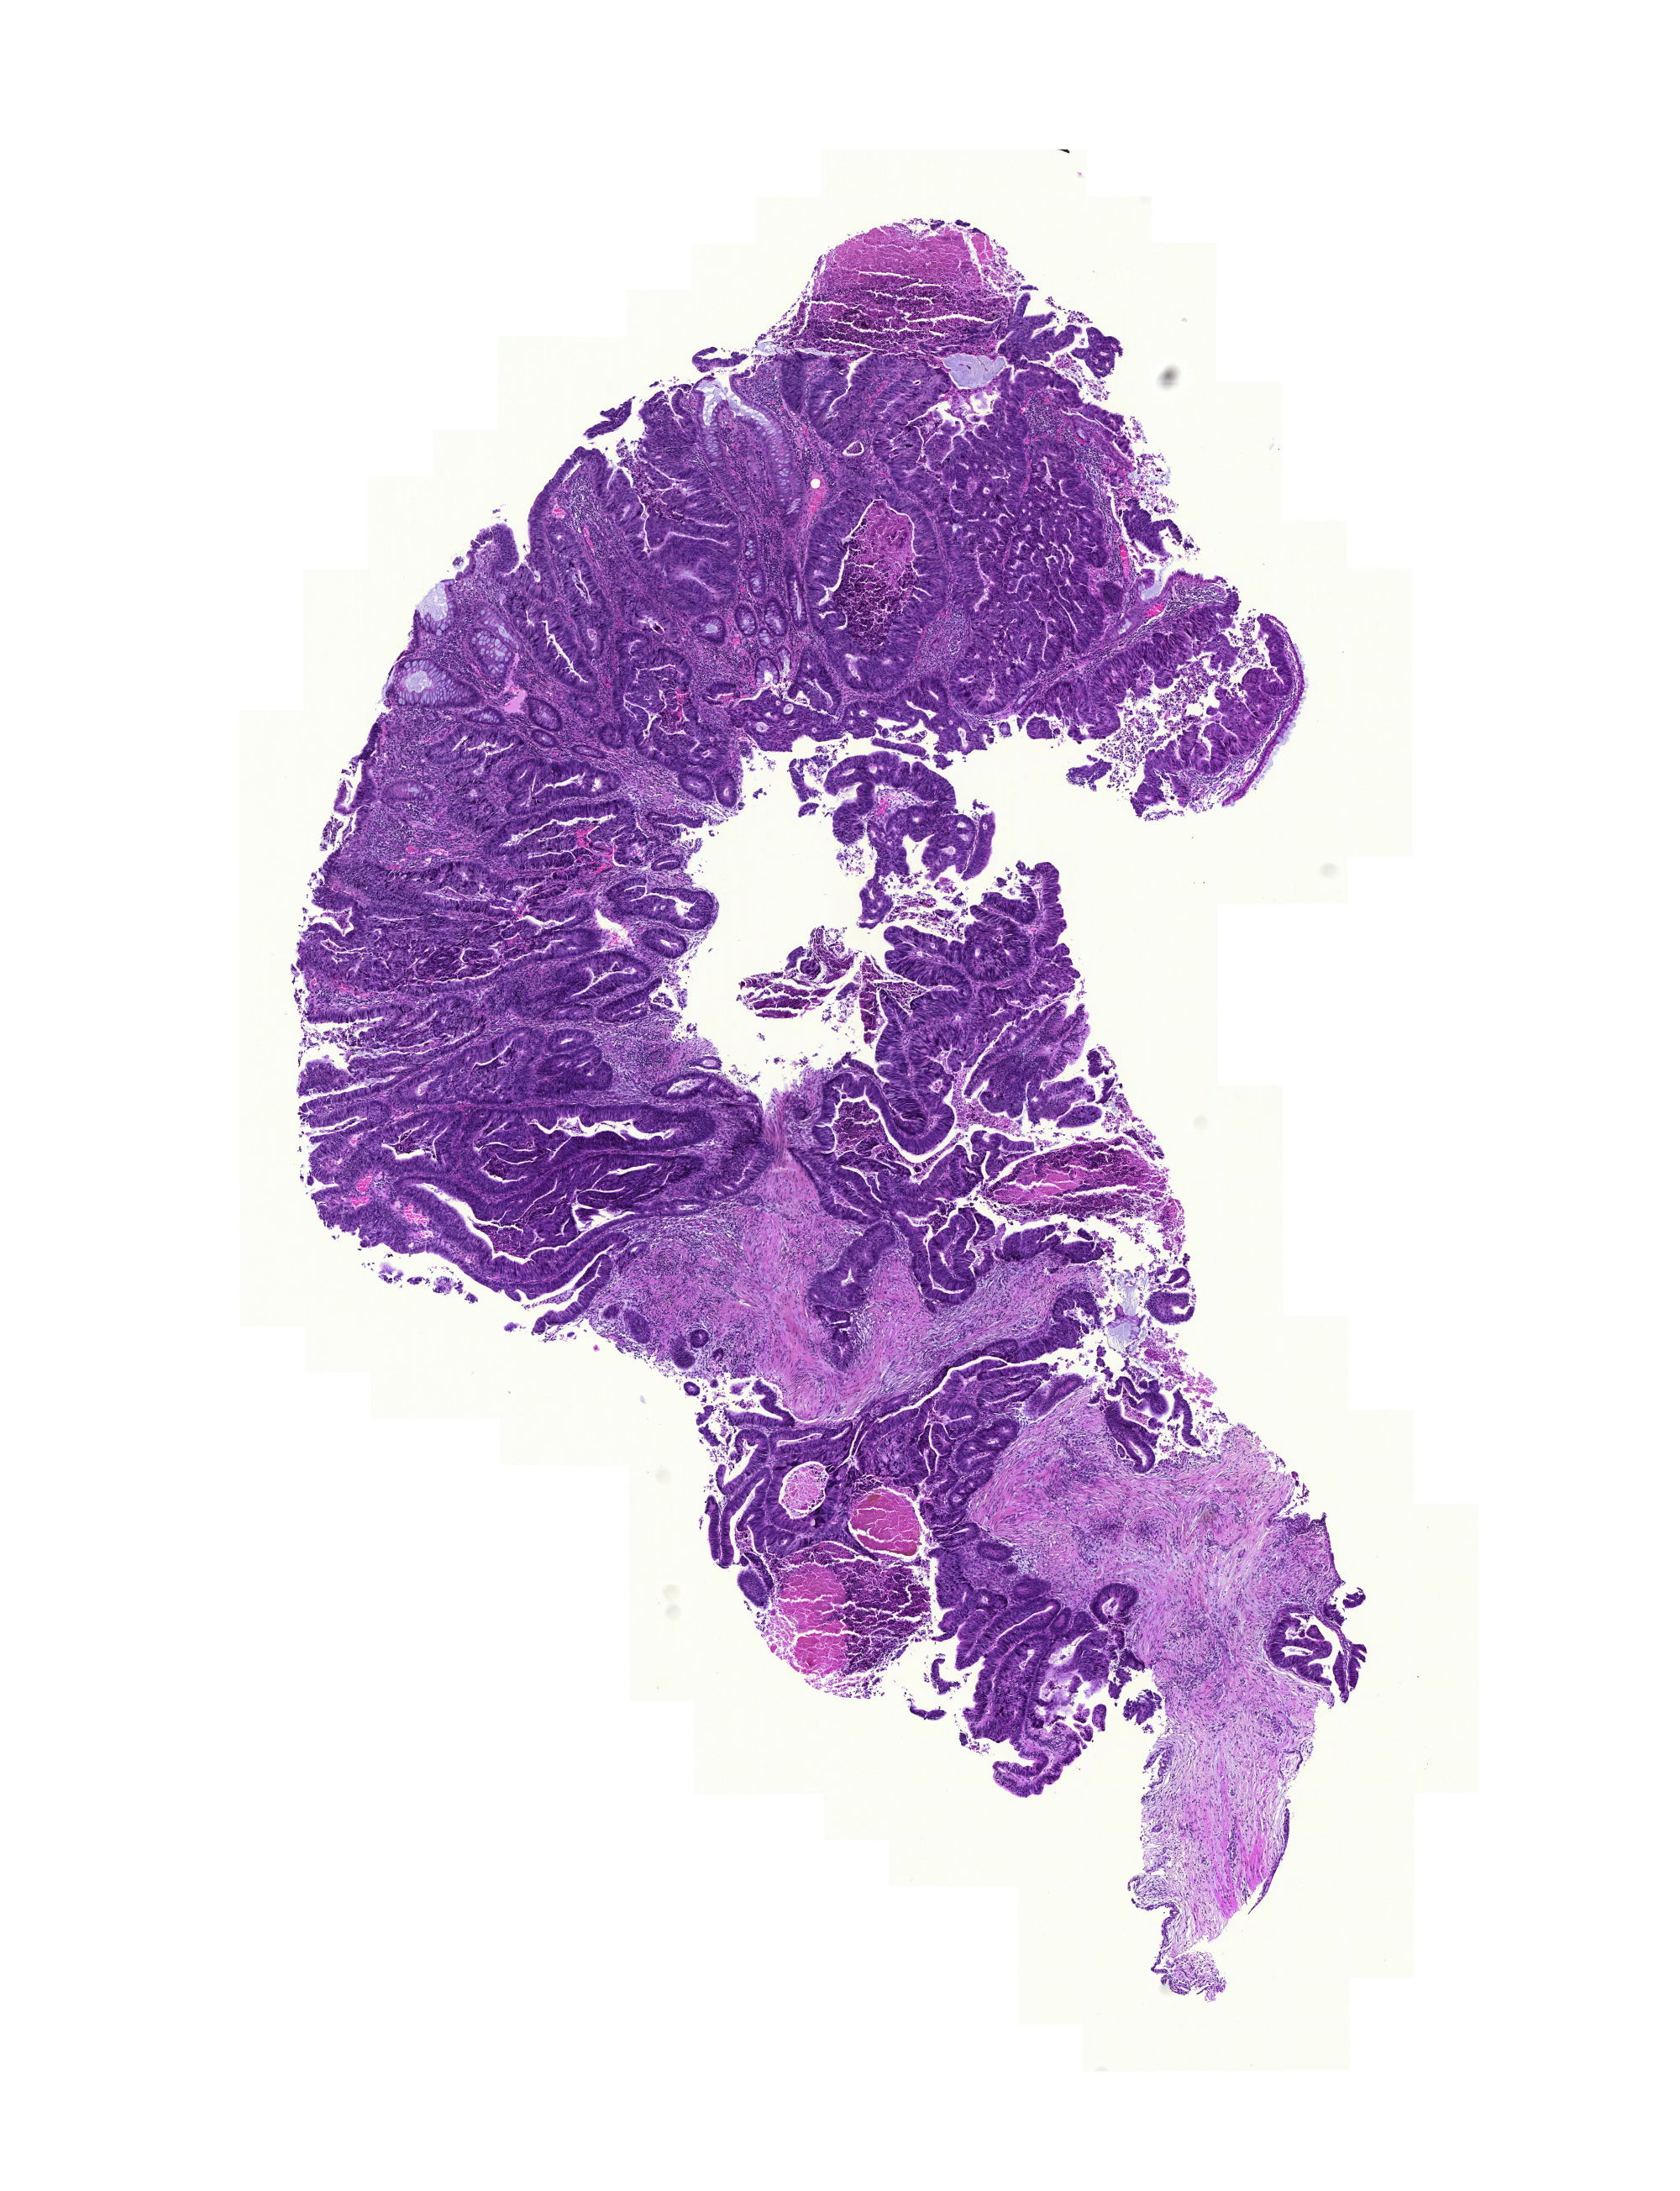
H&E whole-slide image, a low-resolution overview of the entire scanned area, about 7.4 x 9.7 mm (from a 20x scan); formalin-fixed paraffin-embedded (FFPE) diagnostic section; primary tumour sample from the colon. Male patient; age at initial diagnosis 70 years.
Lymph nodes positive (case pathology): 0 of 37 examined. AJCC pathologic stage: IIA (6th edition). Diagnosis: Adenocarcinoma, NOS (sigmoid colon).